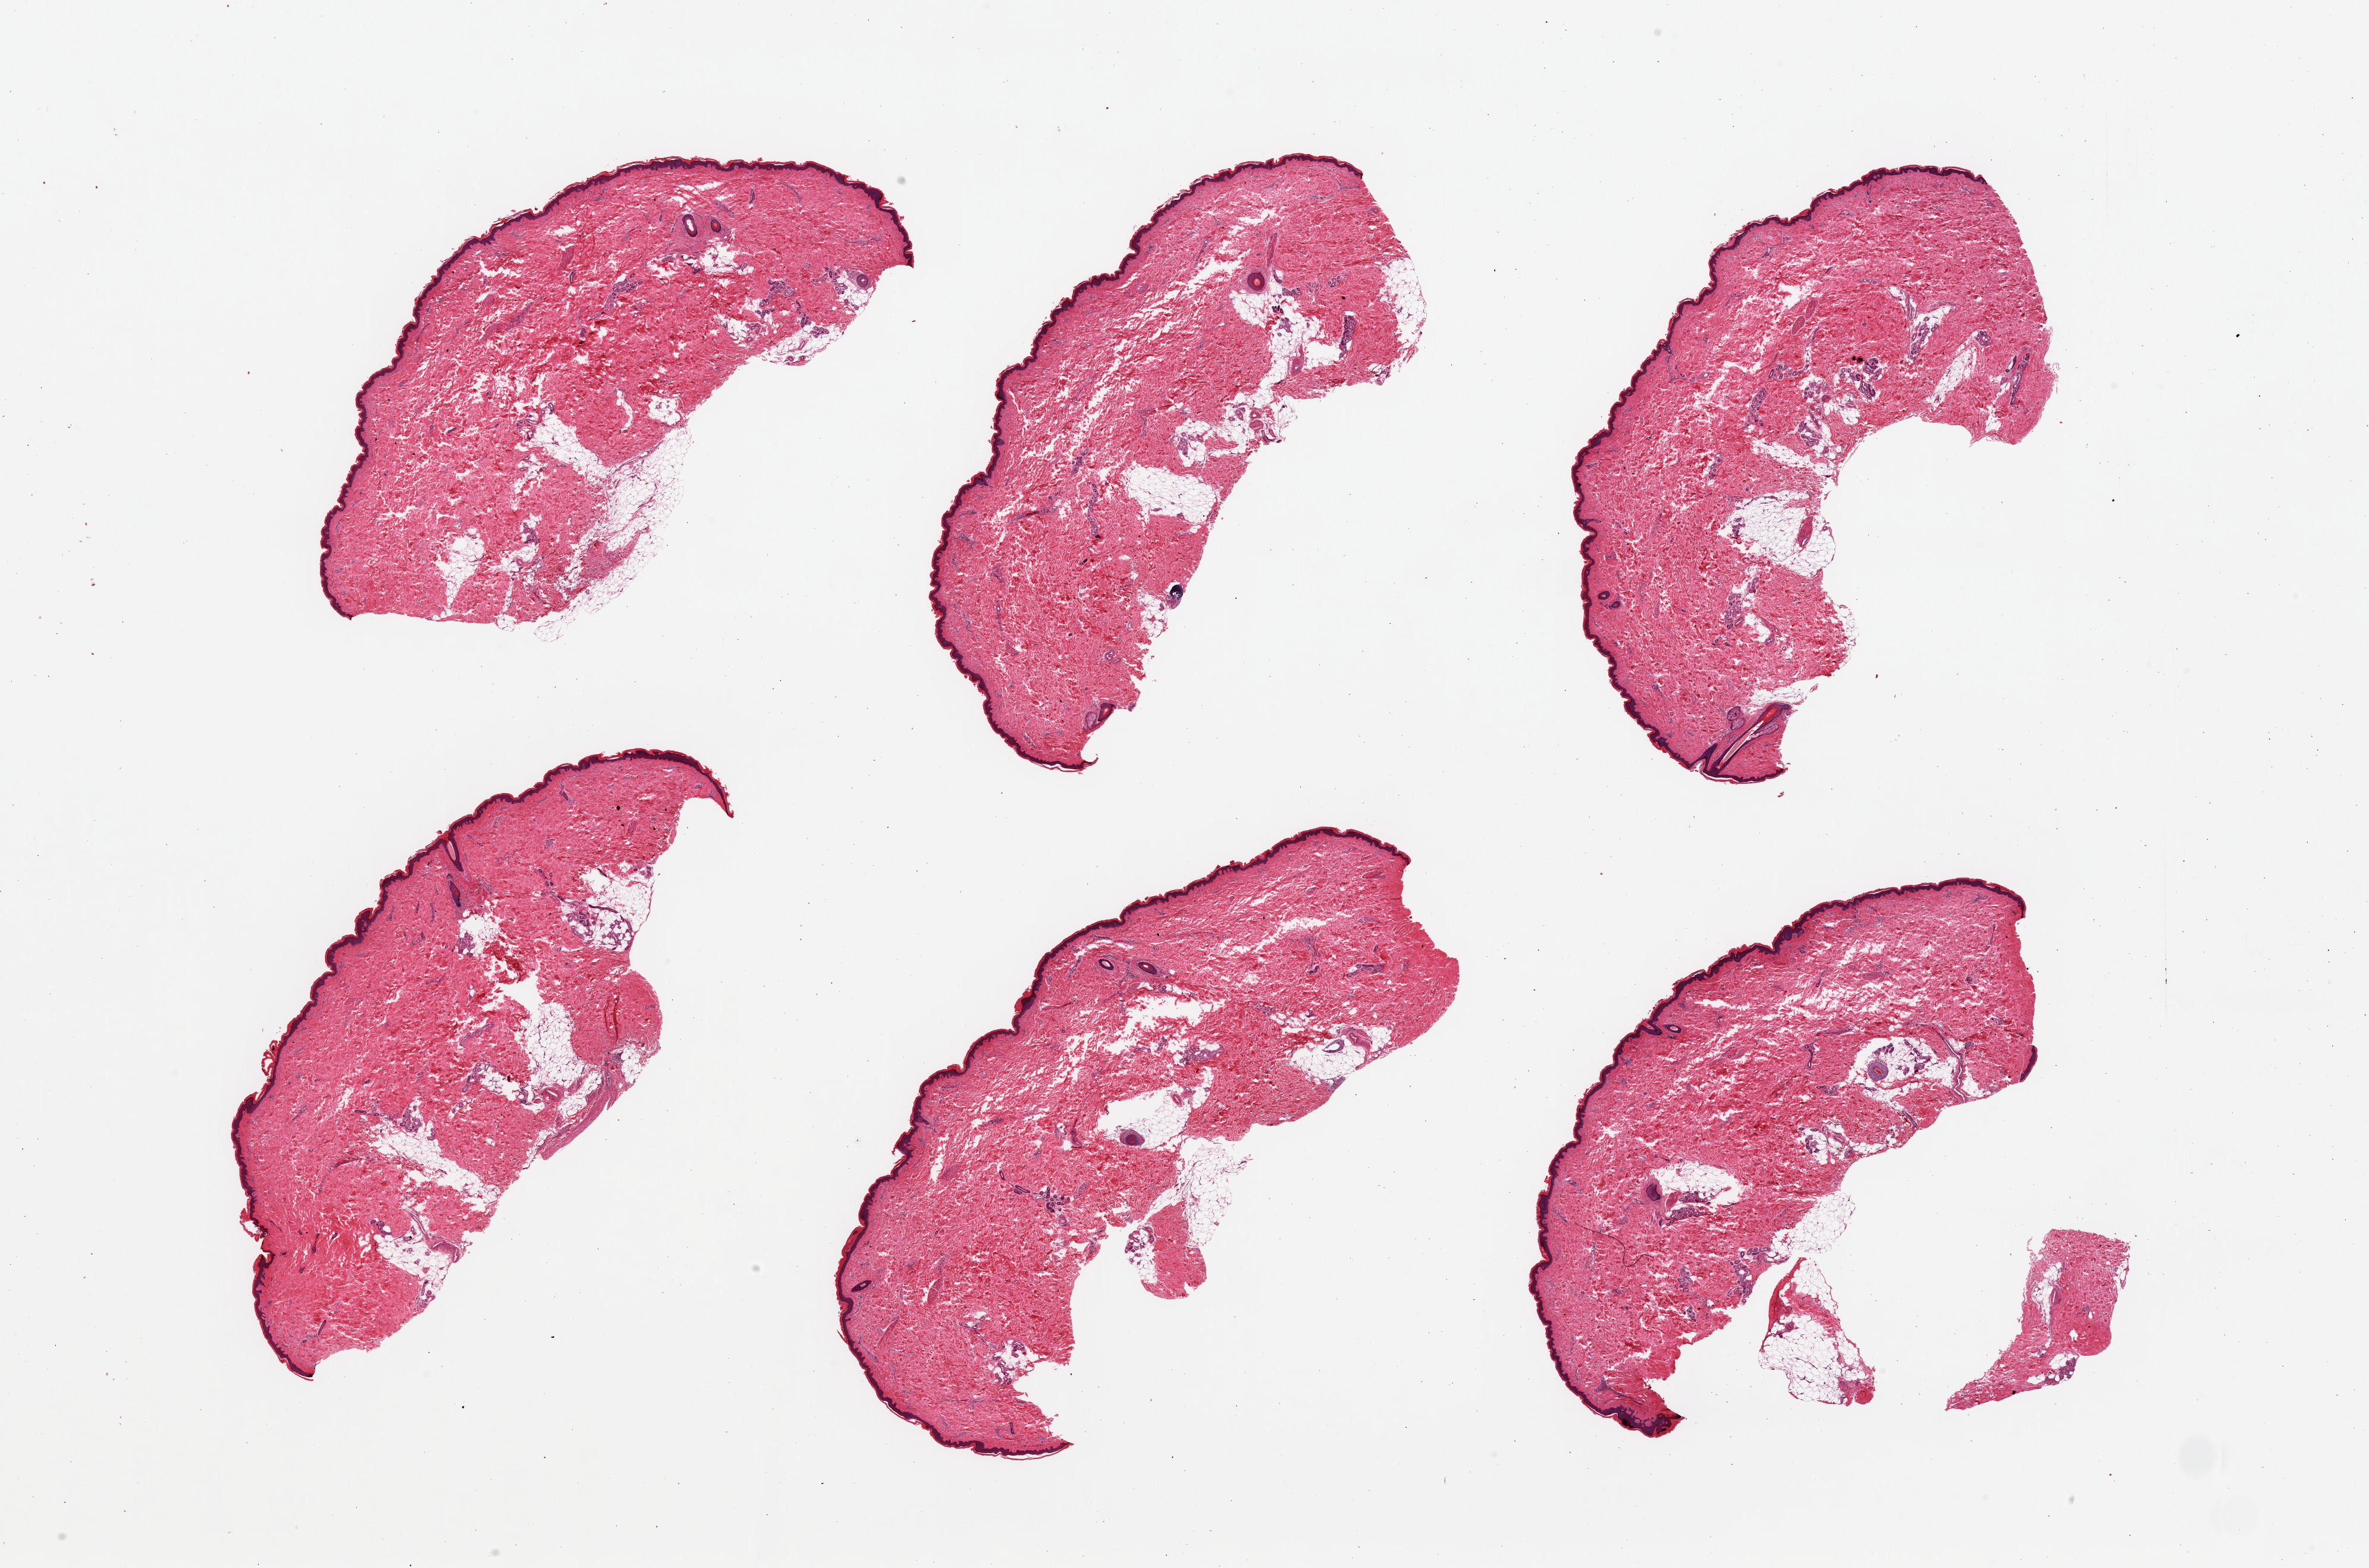
Digitized hematoxylin and eosin (H&E)-stained section, whole scanned area (about 31.5 x 20.9 mm, from a 20x scan) shown as a low-resolution overview. PAXgene-fixed paraffin-embedded (PFPE) section. Target tissue: skin of lower leg. Donor tissue sample. Donor sex: female.
Pathologist's review note for this sample: 6 pieces, mild dermal fat; squamous epithelium up to ~50 microns.